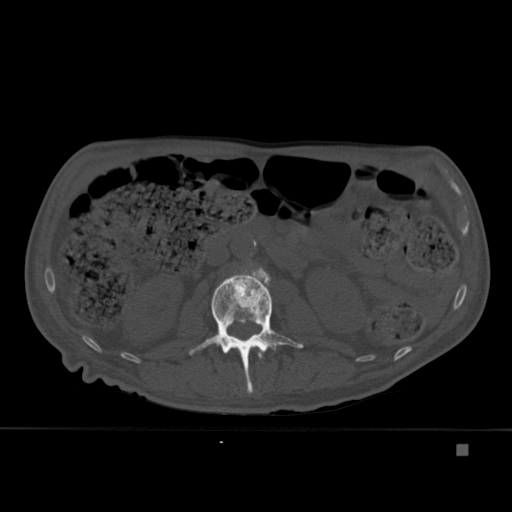
CT including the spine, one axial slice; position 162 of 451 along the scan axis; bone window (W 1800 / L 400 HU); 1.5 mm slice thickness; 512 × 512 image matrix, field of view 378 × 378 mm. Male patient, age 75 years. From the clinical record (not read from this slice): primary cancer: prostate.
Structures marked on this image (semi-automatically segmented with operator editing):
- L1 vertebra: bounding box <258,350,263,359> (left, top, right, bottom; pixels)
- L2 vertebra: <189,267,304,394>